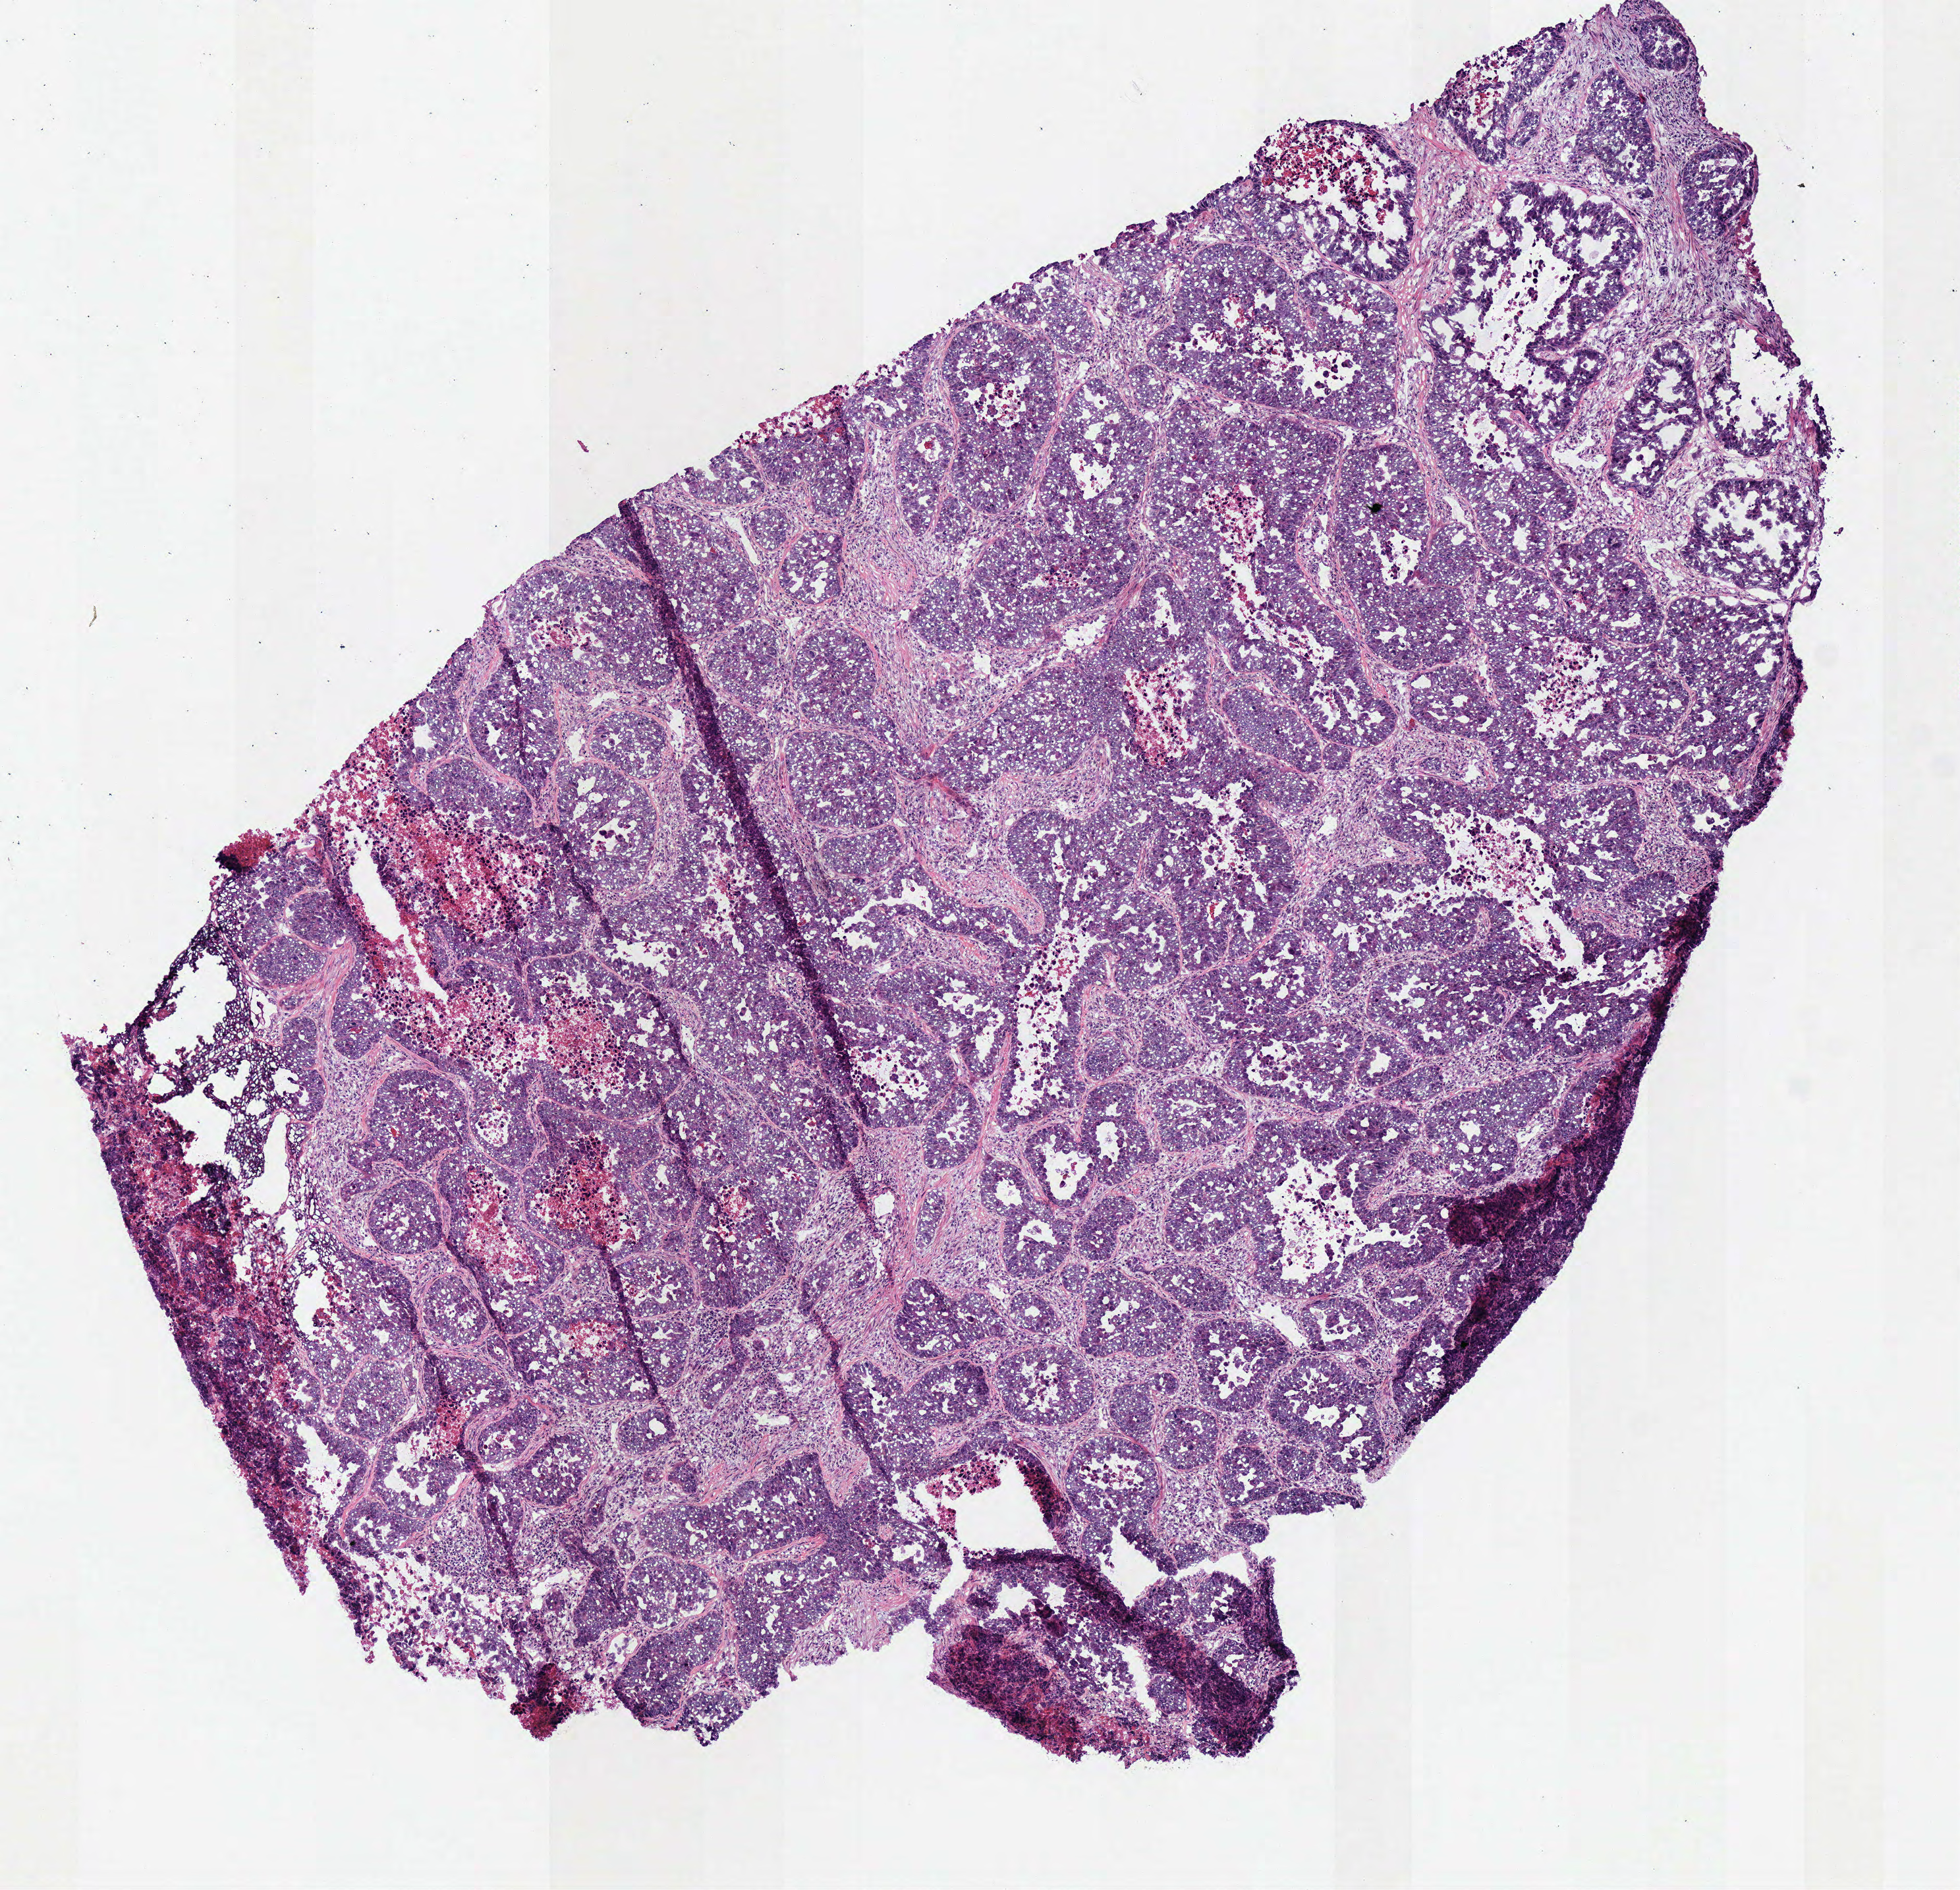
Hematoxylin and eosin (H&E) stained whole-slide image — shown as a low-resolution overview of the whole scanned area (about 5.9 x 5.6 mm, slide scanned at 40x). Frozen section from the bottom of the tissue portion. Sample: primary tumour, lung. Patient: female, age at initial diagnosis 62 years. Composition of this section per pathologist review: tumour cells 70%, tumour nuclei 70%, normal cells 0%, stromal cells 10%, necrosis 20%.
TNM: T2 N0 MX. AJCC pathologic stage: IB (5th edition). Pathologic diagnosis: Adenocarcinoma, NOS (lower lobe, lung).